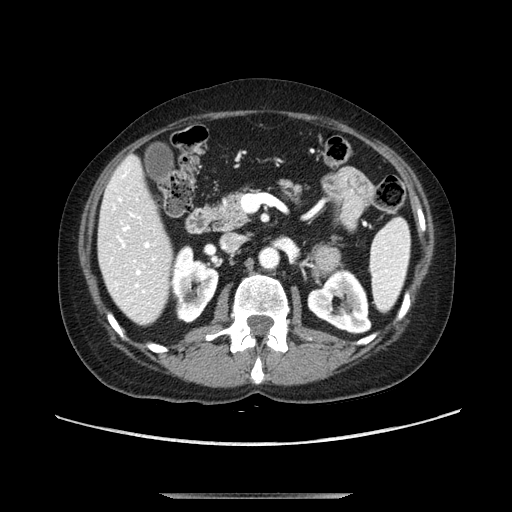
Contrast-enhanced abdominal CT, one axial slice; position 53 of 107 along the scan axis; soft-tissue window (W 400 / L 40 HU); 2.5 mm slice thickness; 512 × 512 image matrix. Female patient. From the clinical record (not read from this slice): diagnosis: adrenocortical carcinoma; tumour side: left adrenal; tumour size at pathology: 7.5 cm; Ki-67 index: 9 %; stage (as recorded): 3.
Annotated regions visible in this slice (semi-automatically segmented with operator editing):
- mass: box from (x=311, y=244) to (x=341, y=279) px